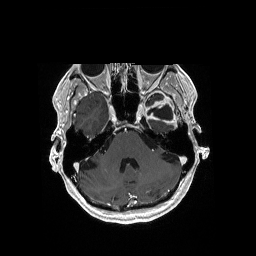
Brain MRI from a brain-tumour surgery series, one axial slice; T1-weighted post-contrast; 1 mm slice thickness; 256 × 256 image matrix, field of view 256 × 256 mm. Case-level facts recorded for this patient, not image findings: histopathology: Glioblastoma; WHO grade: 4.
Structures marked on this image (outlined manually by an expert reader):
- previous resection cavity: bounding box (x1, y1, x2, y2) in pixels: (148, 105, 173, 119)
- tumour: (173, 121, 176, 125)